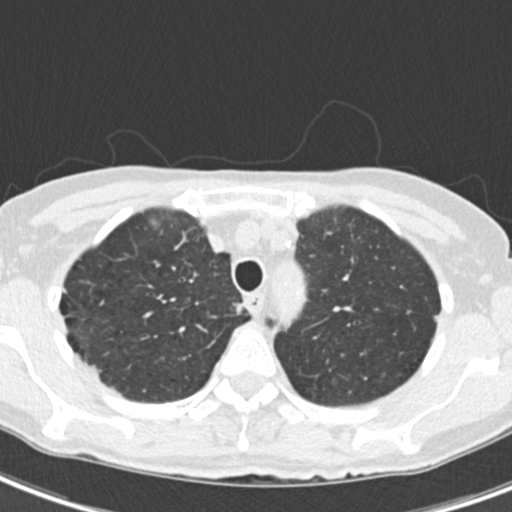
Chest CT (low-dose screening protocol), one axial image, second annual screen, lung window (W 1500 / L -600 HU), 2 mm slice thickness, 120 kVp, slice 42 of 218 in the series, 512 × 512 image matrix, field of view 286 × 286 mm. Female participant, aged 68 years at enrolment. Current smoker at enrolment.
• Expert-annotated lung lesion, bounding box <229,300,253,323> (left, top, right, bottom; pixels).
• Screening reader's record for this exam: no non-calcified nodule ≥4 mm recorded.
• Official screen result: negative screen, no significant abnormalities.
• Participant outcome: lung cancer diagnosed 436 days after this screen — squamous cell carcinoma, NOS, right upper lobe, mediastinum, poorly differentiated (G3), stage IIIB (AJCC 6th edition), 43 mm at pathology.